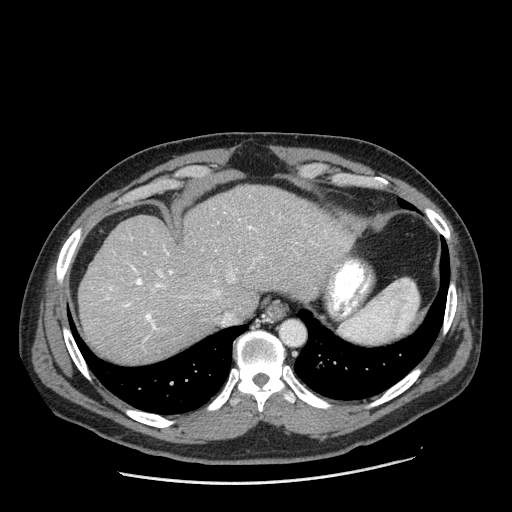
Contrast-enhanced abdominal CT (liver protocol), one axial slice. Slice 155 of 198 in the series (ordered by position). One of 2 acquisitions stored at this slice position. Soft-tissue window (W 400 / L 40 HU). 512 × 512 image matrix, field of view 400 × 400 mm. From the clinical record (not read from this slice): diagnosis: hepatocellular carcinoma (patient treated with transarterial chemoembolisation; whether this scan precedes or follows treatment is not stated here); TNM stage (as recorded): Stage-II; Child-Pugh class: A; tumour differentiation: moderately differentiated; tumour size: 2.6 cm.
Annotated regions visible in this slice (semi-automatic segmentation, software-assisted and operator-edited):
- abdominal aorta: bounding box (x1, y1, x2, y2) in pixels: (281, 321, 303, 344)
- liver parenchyma outside the tumour (the mass and vessels are separate outlines, so this box may not span the whole liver): (78, 184, 354, 362)
- liver vessels: (105, 219, 254, 341)